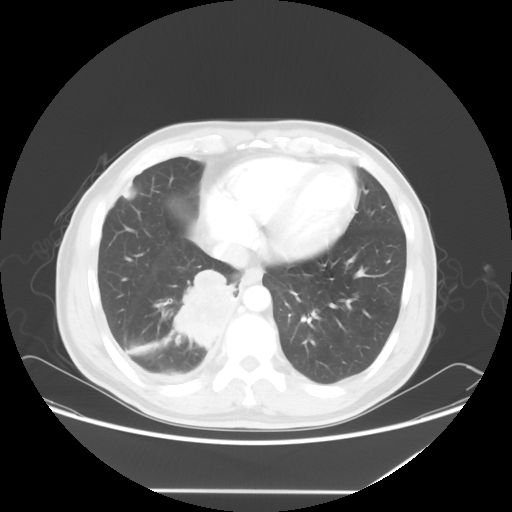
Chest CT, one axial slice. Position 18 of 60 along the scan axis. 120 kVp. Lung window (W 1500 / L -600 HU). 5 mm slice thickness. 512 × 512 image matrix, field of view 419 × 419 mm. Patient: male, 48 years. Case-level facts recorded for this patient, not image findings: clinical TNM (as recorded): T3 N3 M1a.
Outlined on this slice (bounding box drawn by a radiologist):
- lung tumour (recorded histology: squamous cell carcinoma): bounding box [x1, y1, x2, y2] px = [169, 264, 241, 354]